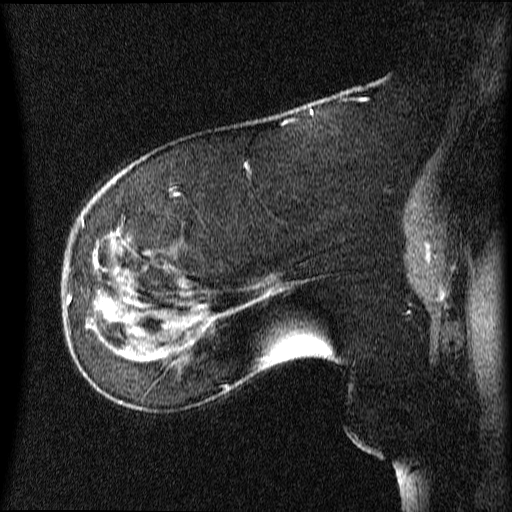
Breast MRI (dynamic contrast-enhanced), one sagittal slice; slice 23 of 64 in the series (ordered by position); dynamic contrast-enhanced series, image 2 of 4 at this slice position (ordered by acquisition); 1.5 T; TE 4.2 ms, TR 9 ms; 2 mm slice thickness; 512 × 512 image matrix, field of view 200 × 200 mm. Patient: female, 63 years.
Outlined on this slice (semi-automatic segmentation, software-assisted and operator-edited):
- analysis volume of interest (the breast-tissue region the enhancement analysis was run in; not a lesion): box from (x=66, y=272) to (x=131, y=353) px
- tumour enhancement mask (voxels above the 70 % enhancement threshold inside the analysis volume of interest): (x=67, y=292)–(x=131, y=353)